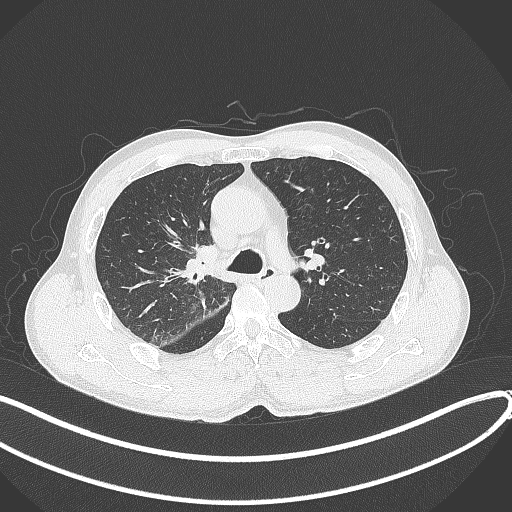
Chest CT, one axial slice. Reconstruction kernel B70f. 120 kVp. Lung window (W 1500 / L -600 HU). 512 × 512 image matrix, field of view 400 × 400 mm. Male patient, age 53 years. Case-level facts recorded for this patient, not image findings: clinical TNM (as recorded): T1b N0 M0.
Outlined on this slice (rectangle marked by the reading radiologist):
- lung tumour (recorded histology: squamous cell carcinoma): bounding box (x1, y1, x2, y2) in pixels: (180, 238, 224, 287)